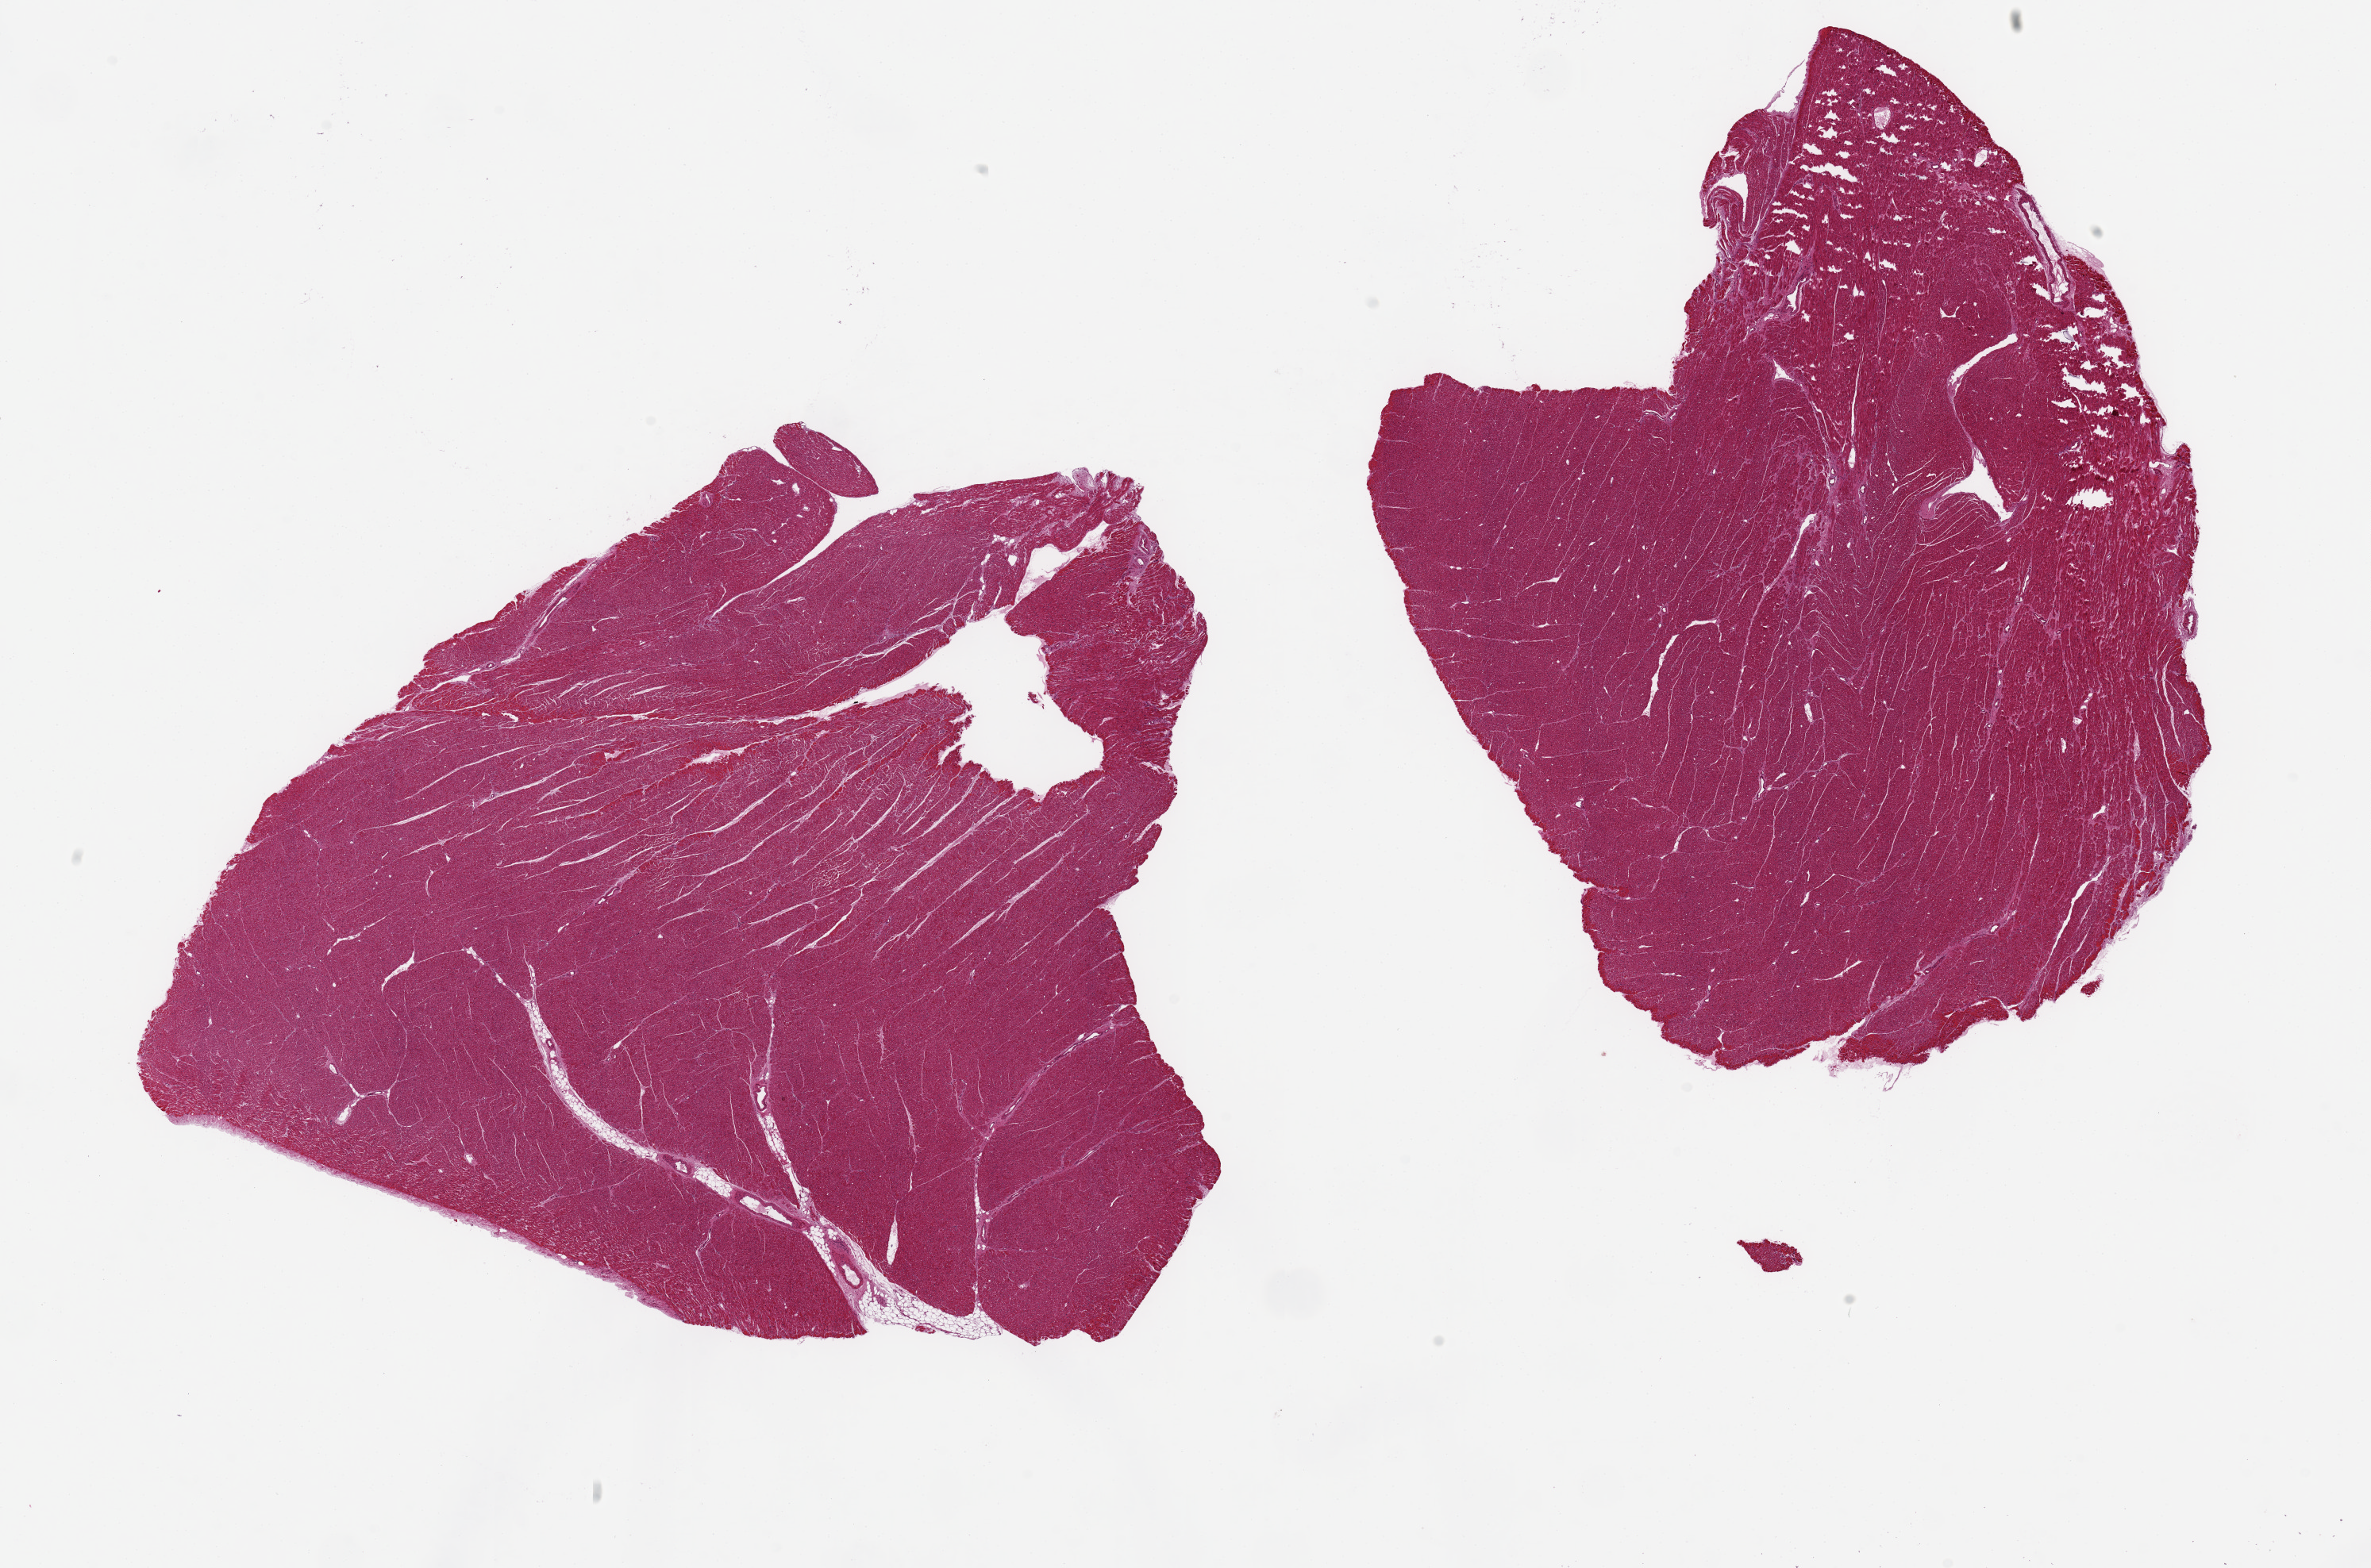
Digitized H&E-stained section, a low-resolution overview of the entire scanned area, about 23.6 x 15.6 mm. PAXgene-fixed, paraffin-embedded tissue. Section of heart (target tissue). Tissue donor sample. Donor sex: male.
Pathologist's review note for this sample: 2 pieces 10x9 & 8x8 mm; minimal adipose.